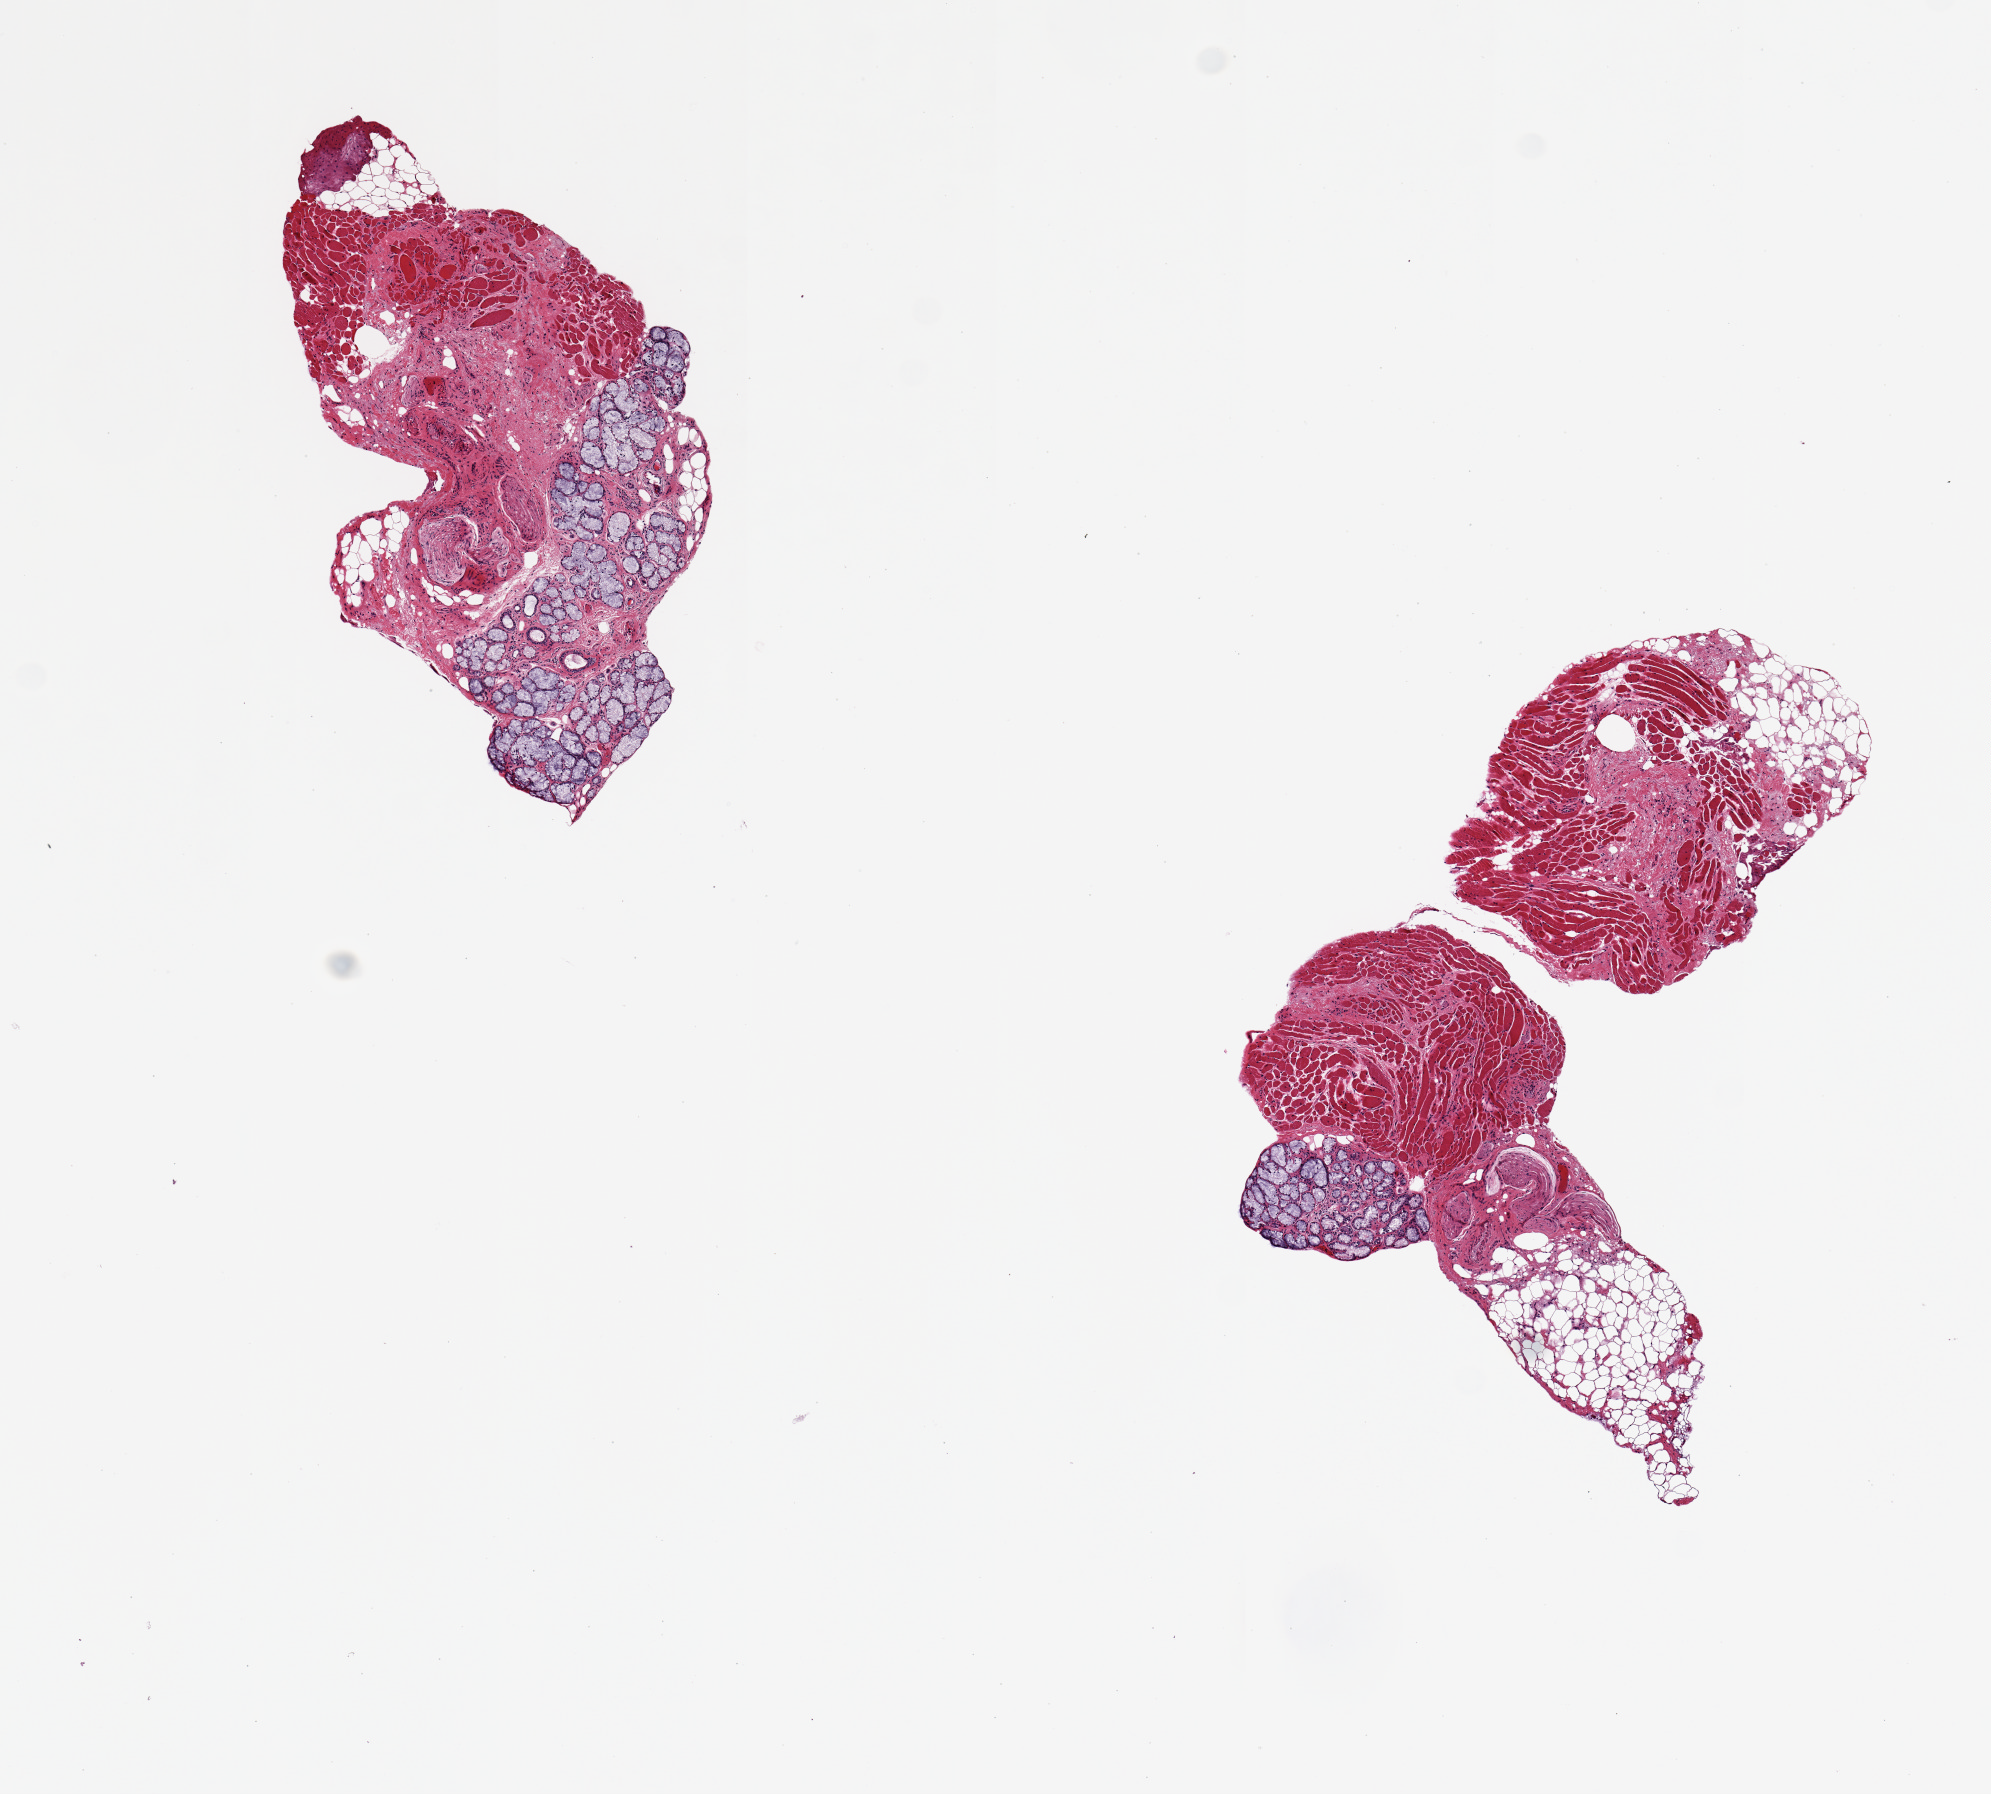
Whole-slide image, H&E stain, shown as a low-resolution overview of the whole scanned area (about 7.9 x 7.1 mm, acquisition: 20x scan), PAXgene-fixed paraffin-embedded (PFPE) section, sampled site (target tissue): minor salivary gland, tissue donor sample.
- pathologist's review note for this sample: 3 pieces: 1, 50% gland, 50% muscle; 1, 20% gland, 80% fat and muscle; 1, all muscle (images labeled)